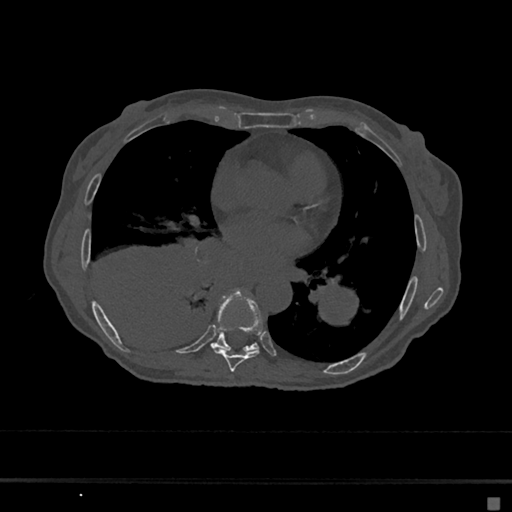
CT including the spine, one axial slice; reconstruction kernel Br40s/3; 120 kVp; bone window (W 1800 / L 400 HU); 0.5 mm slice thickness; 512 × 512 image matrix, field of view 360 × 360 mm. Patient: female, 68 years. Case-level facts recorded for this patient, not image findings: primary cancer: renal.
Annotated regions visible in this slice (semi-automatic segmentation, software-assisted and operator-edited):
- T7 vertebra: bounding box <213,297,263,372> (left, top, right, bottom; pixels)
- T8 vertebra: <211,290,258,352>